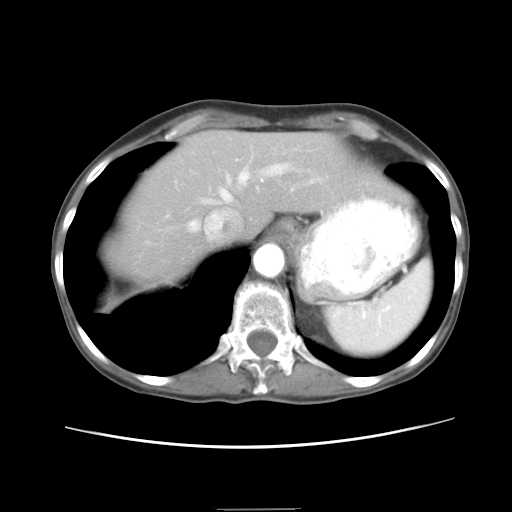
Contrast-enhanced abdominal CT, one axial slice. Position 19 of 26 along the scan axis. Reconstruction kernel STANDARD. 120 kVp. Intravenous contrast given. Soft-tissue window (W 400 / L 40 HU). 7.5 mm slice thickness. 512 × 512 image matrix. Female patient, age 65 years. From the clinical record (not read from this slice): diagnosis: colorectal cancer liver metastases, imaged before liver resection; multiple liver metastases: no; disease in both lobes: yes; chemotherapy before resection: yes.
Outlined on this slice (manually delineated by an expert):
- hepatic veins: bounding box <189,164,288,231> (left, top, right, bottom; pixels)
- liver: <112,132,382,280>
- planned liver remnant (the part of the liver to remain after resection): <112,132,382,280>